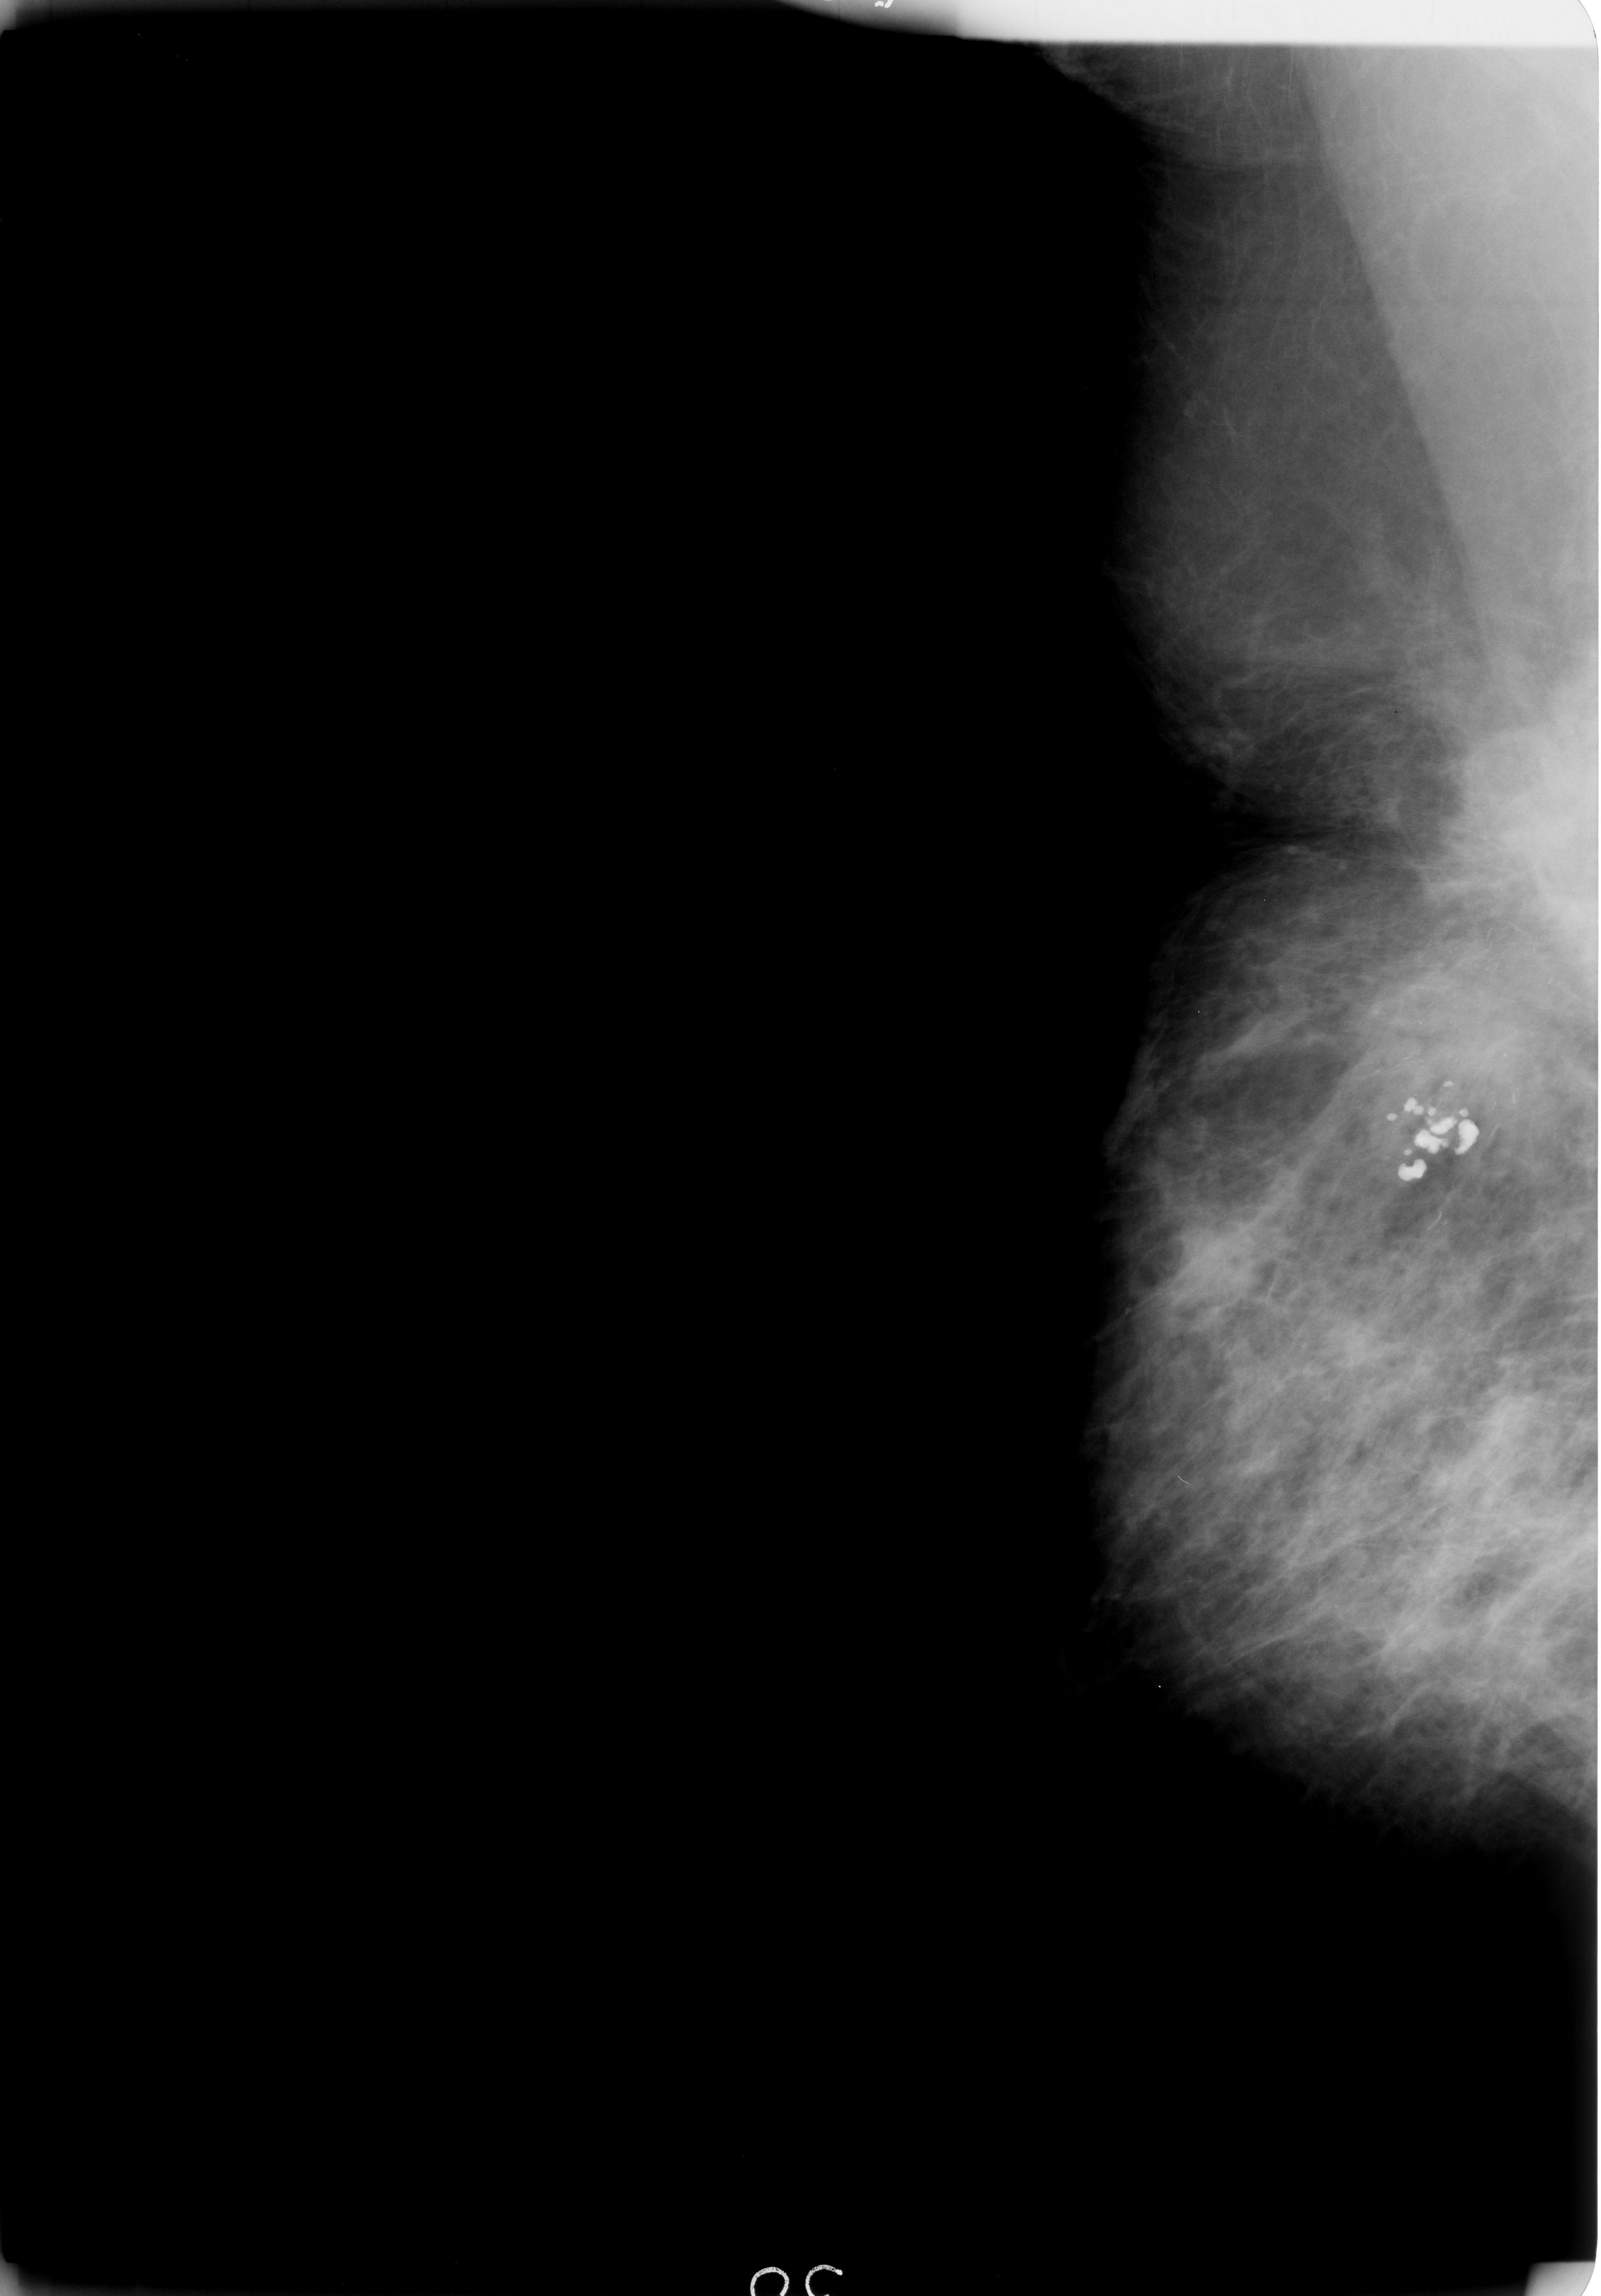
Mammogram (digitized film); right breast; MLO view; BI-RADS breast density category 2 (scale 1–4).
Radiologist-marked abnormalities on this image: mass, shape irregular / architectural distortion, margins ill defined / spiculated; BI-RADS assessment category 5; pathology (as recorded): malignant.